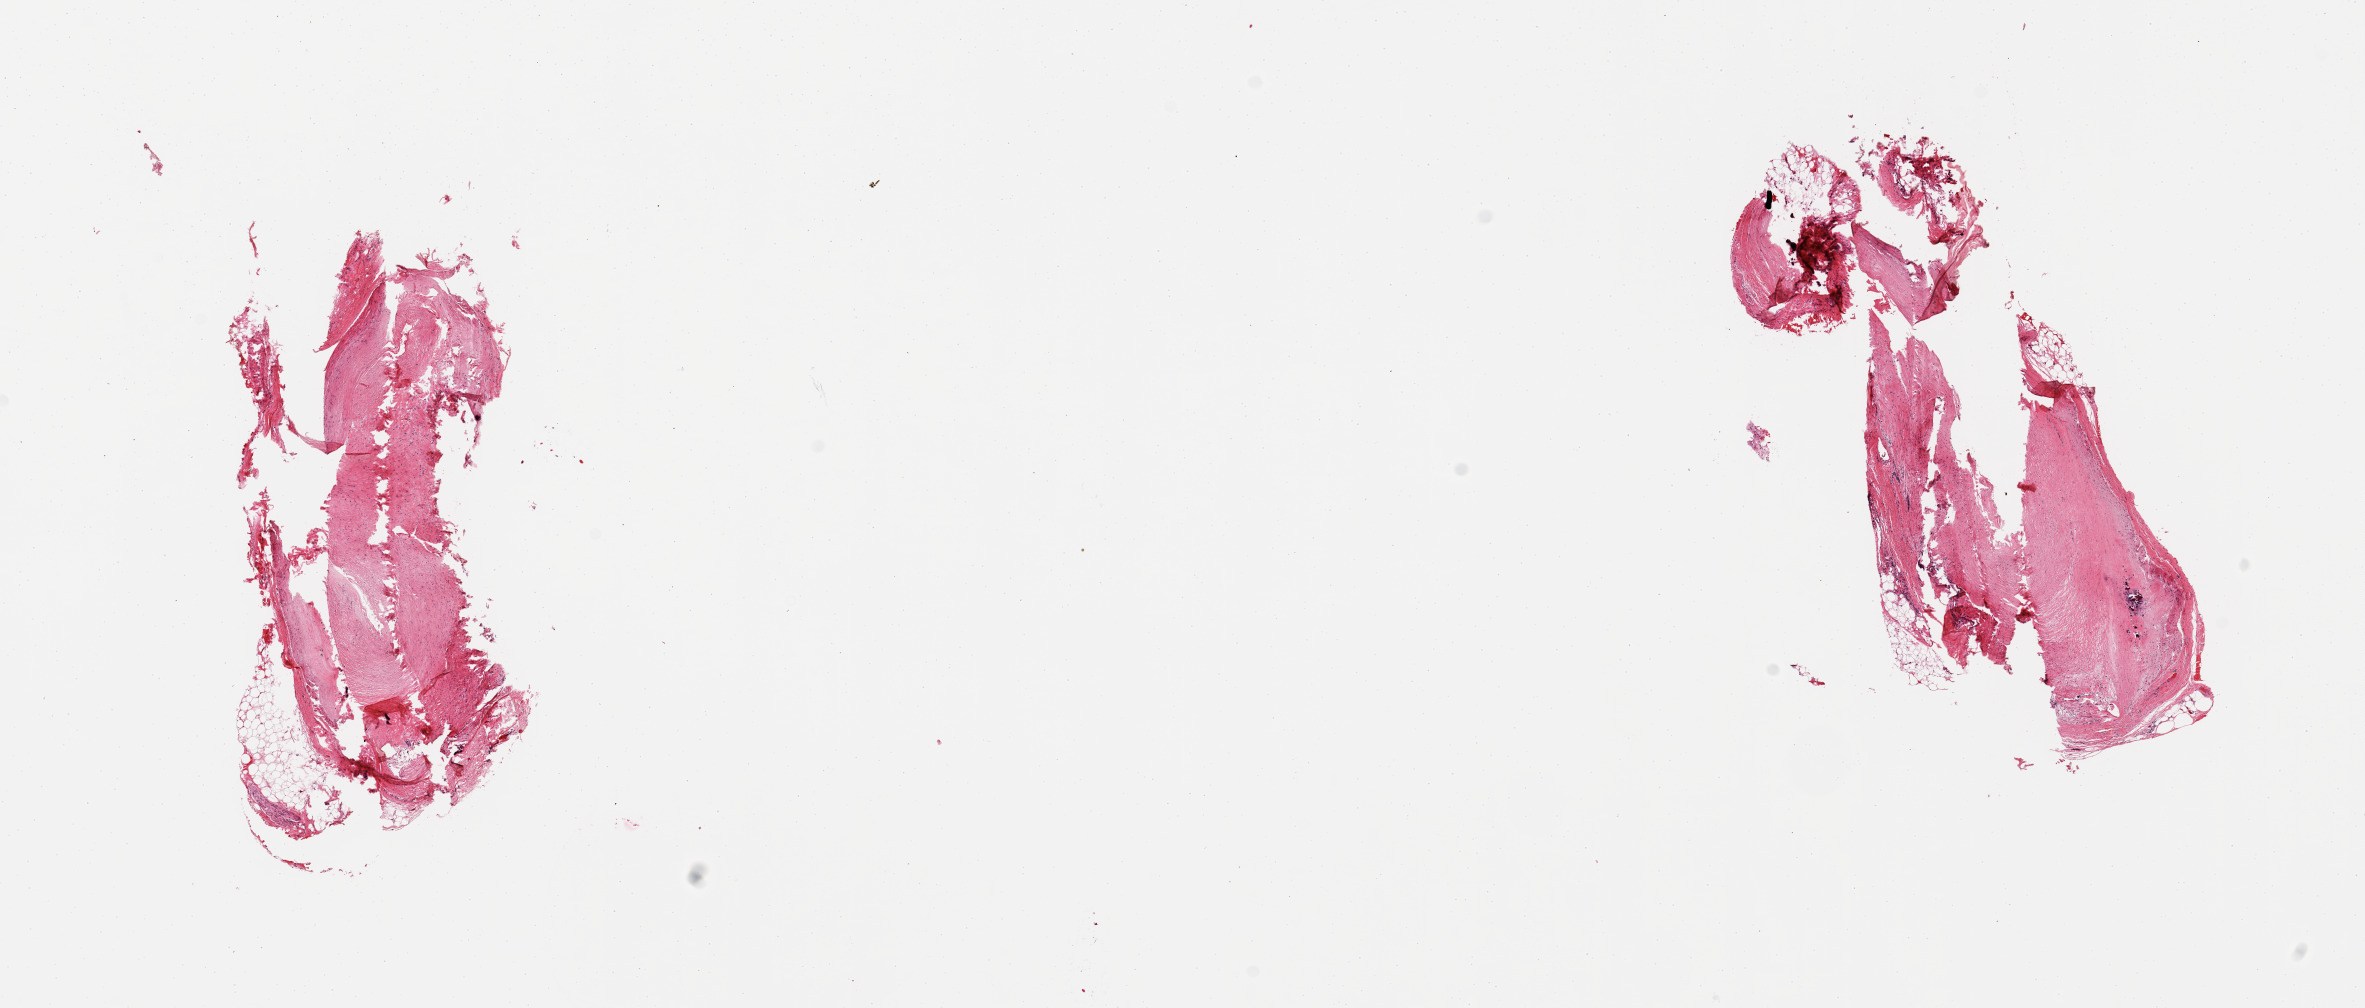
Whole-slide image, hematoxylin and eosin (H&E) stain, a low-resolution overview of the entire scanned area, about 18.7 x 8.0 mm, PAXgene-fixed, paraffin-embedded tissue, target tissue: coronary artery, donor tissue sample.
Review note (as recorded): 2 pieces; fragmented; calcified fibrofatty plaques.